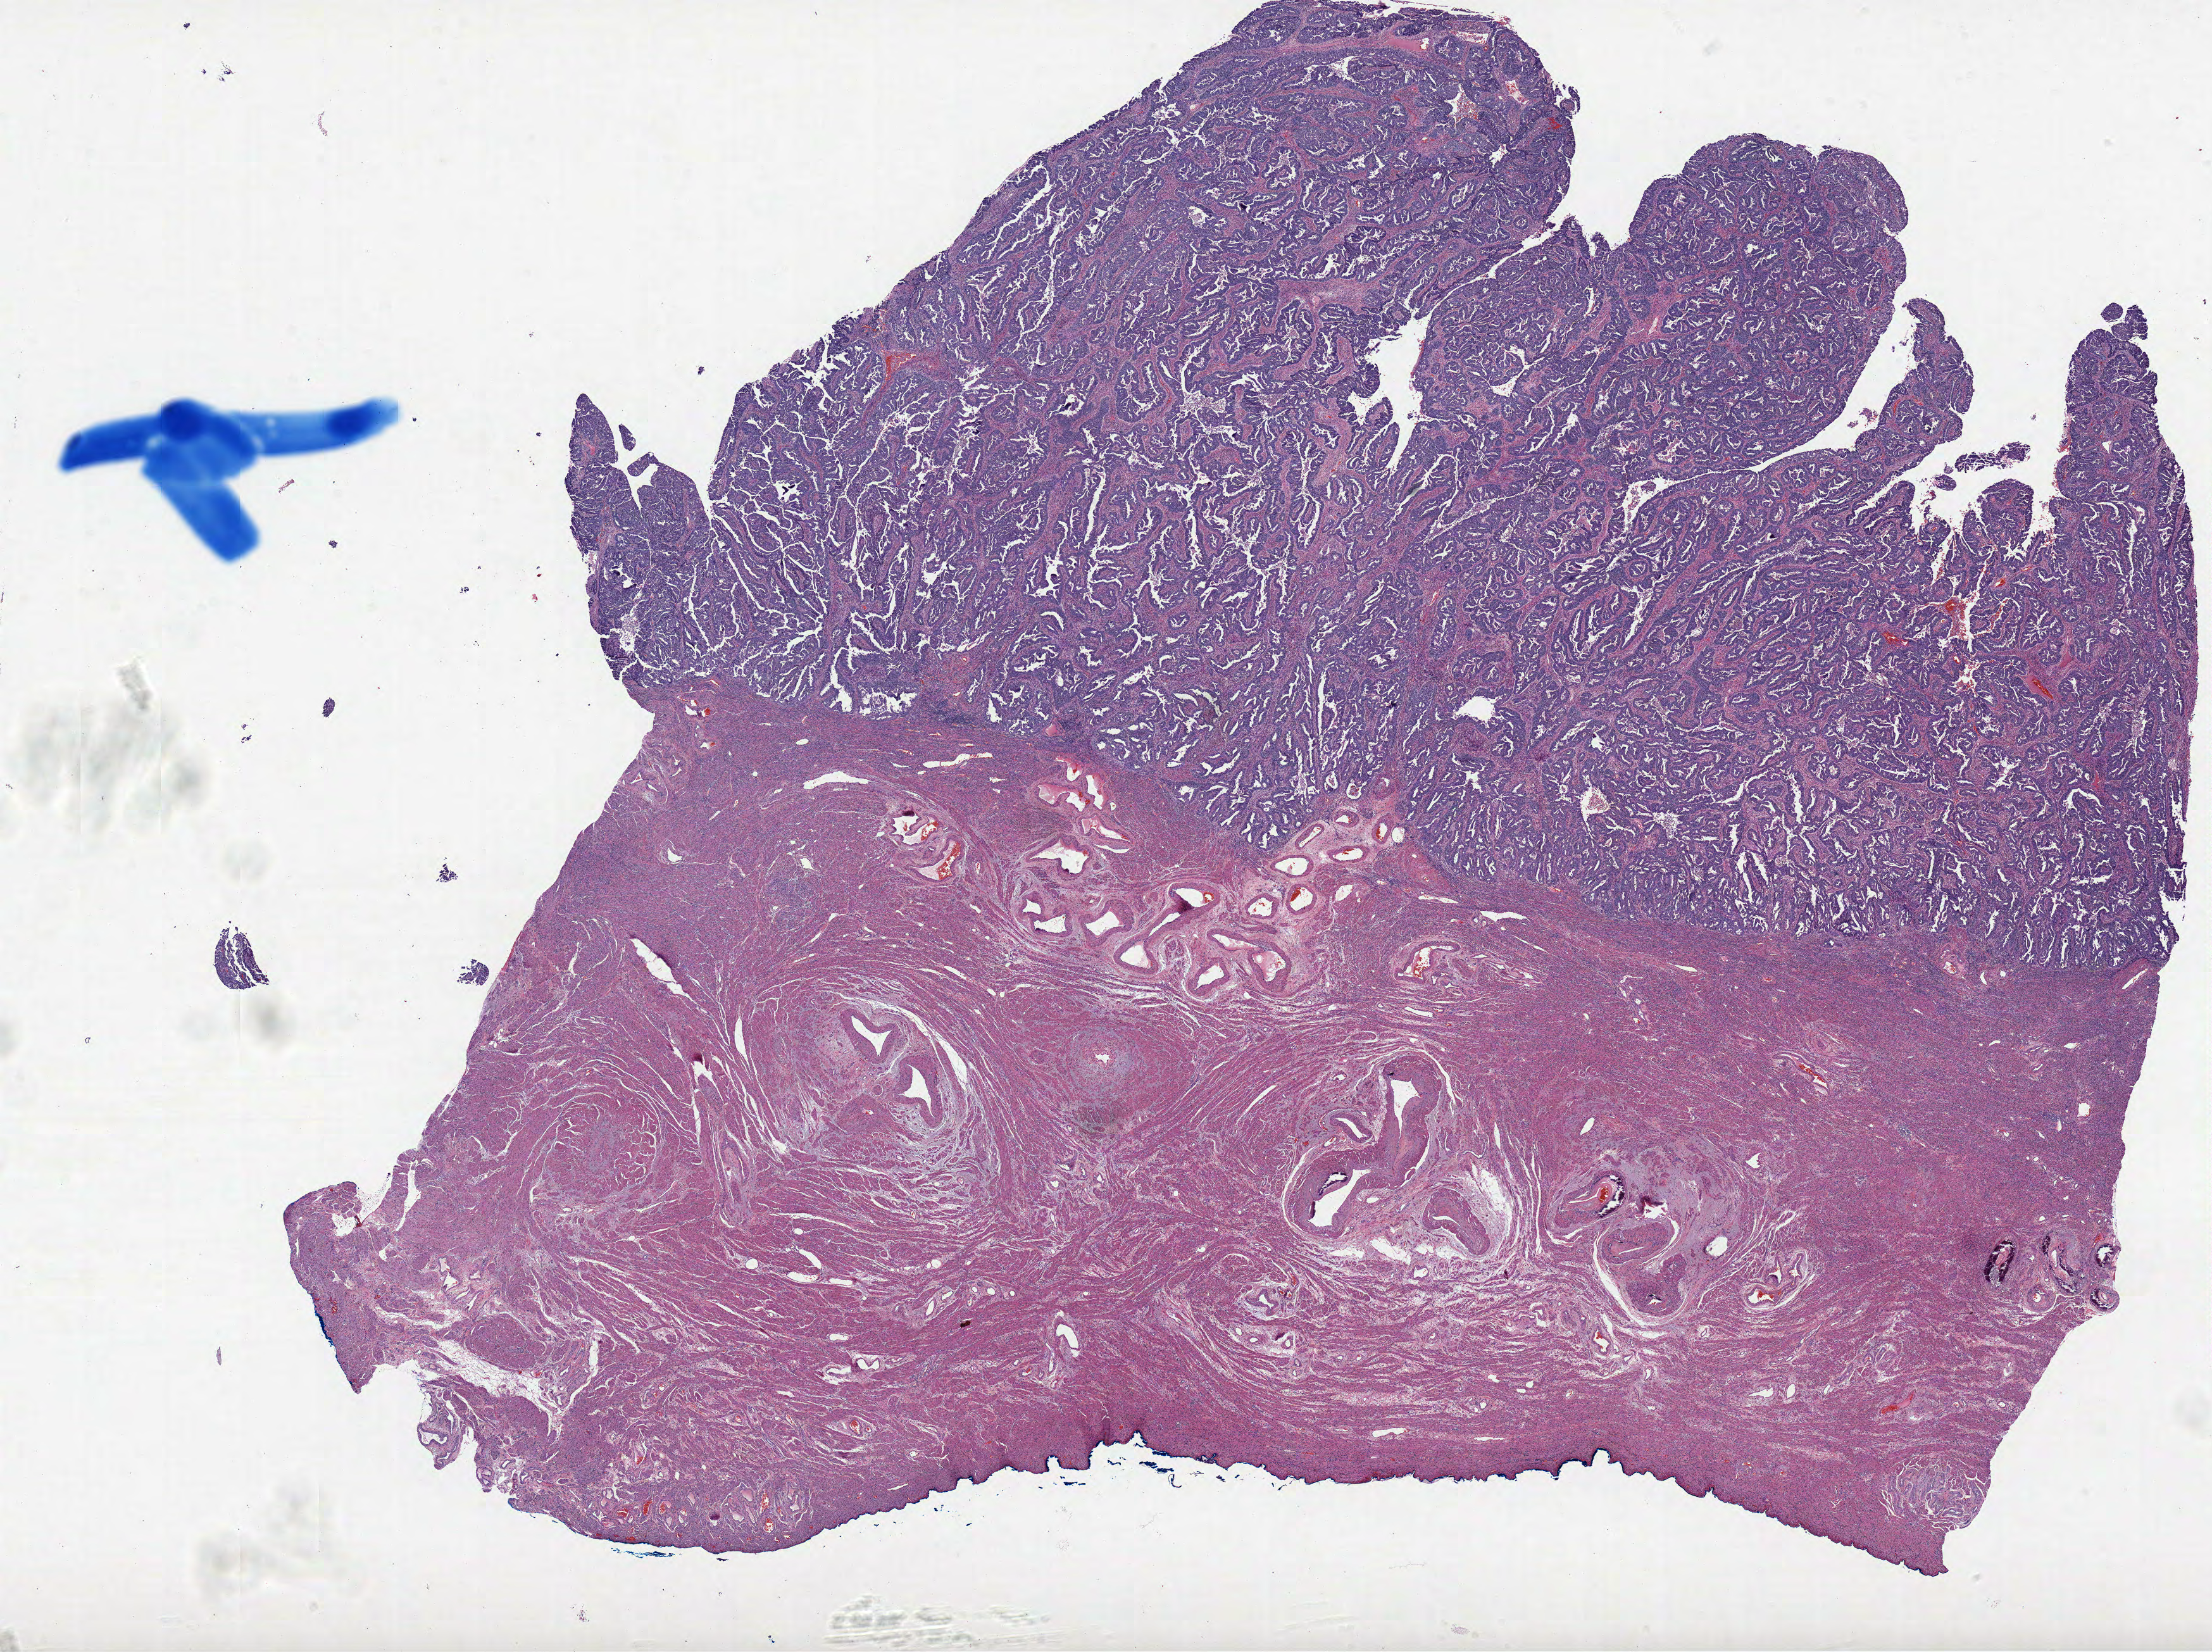
Digitized Hematoxylin and eosin (H&E) stained tissue section (whole slide) — whole scanned area (about 27.8 x 20.8 mm) shown as a low-resolution overview. Formalin-fixed paraffin-embedded (FFPE) diagnostic section. Primary tumour sample from the uterus. Patient: female, age at initial diagnosis 81 years. Histologic grade: G3 (poorly differentiated).
Histologic diagnosis: Serous cystadenocarcinoma, NOS (endometrium). FIGO stage: II.